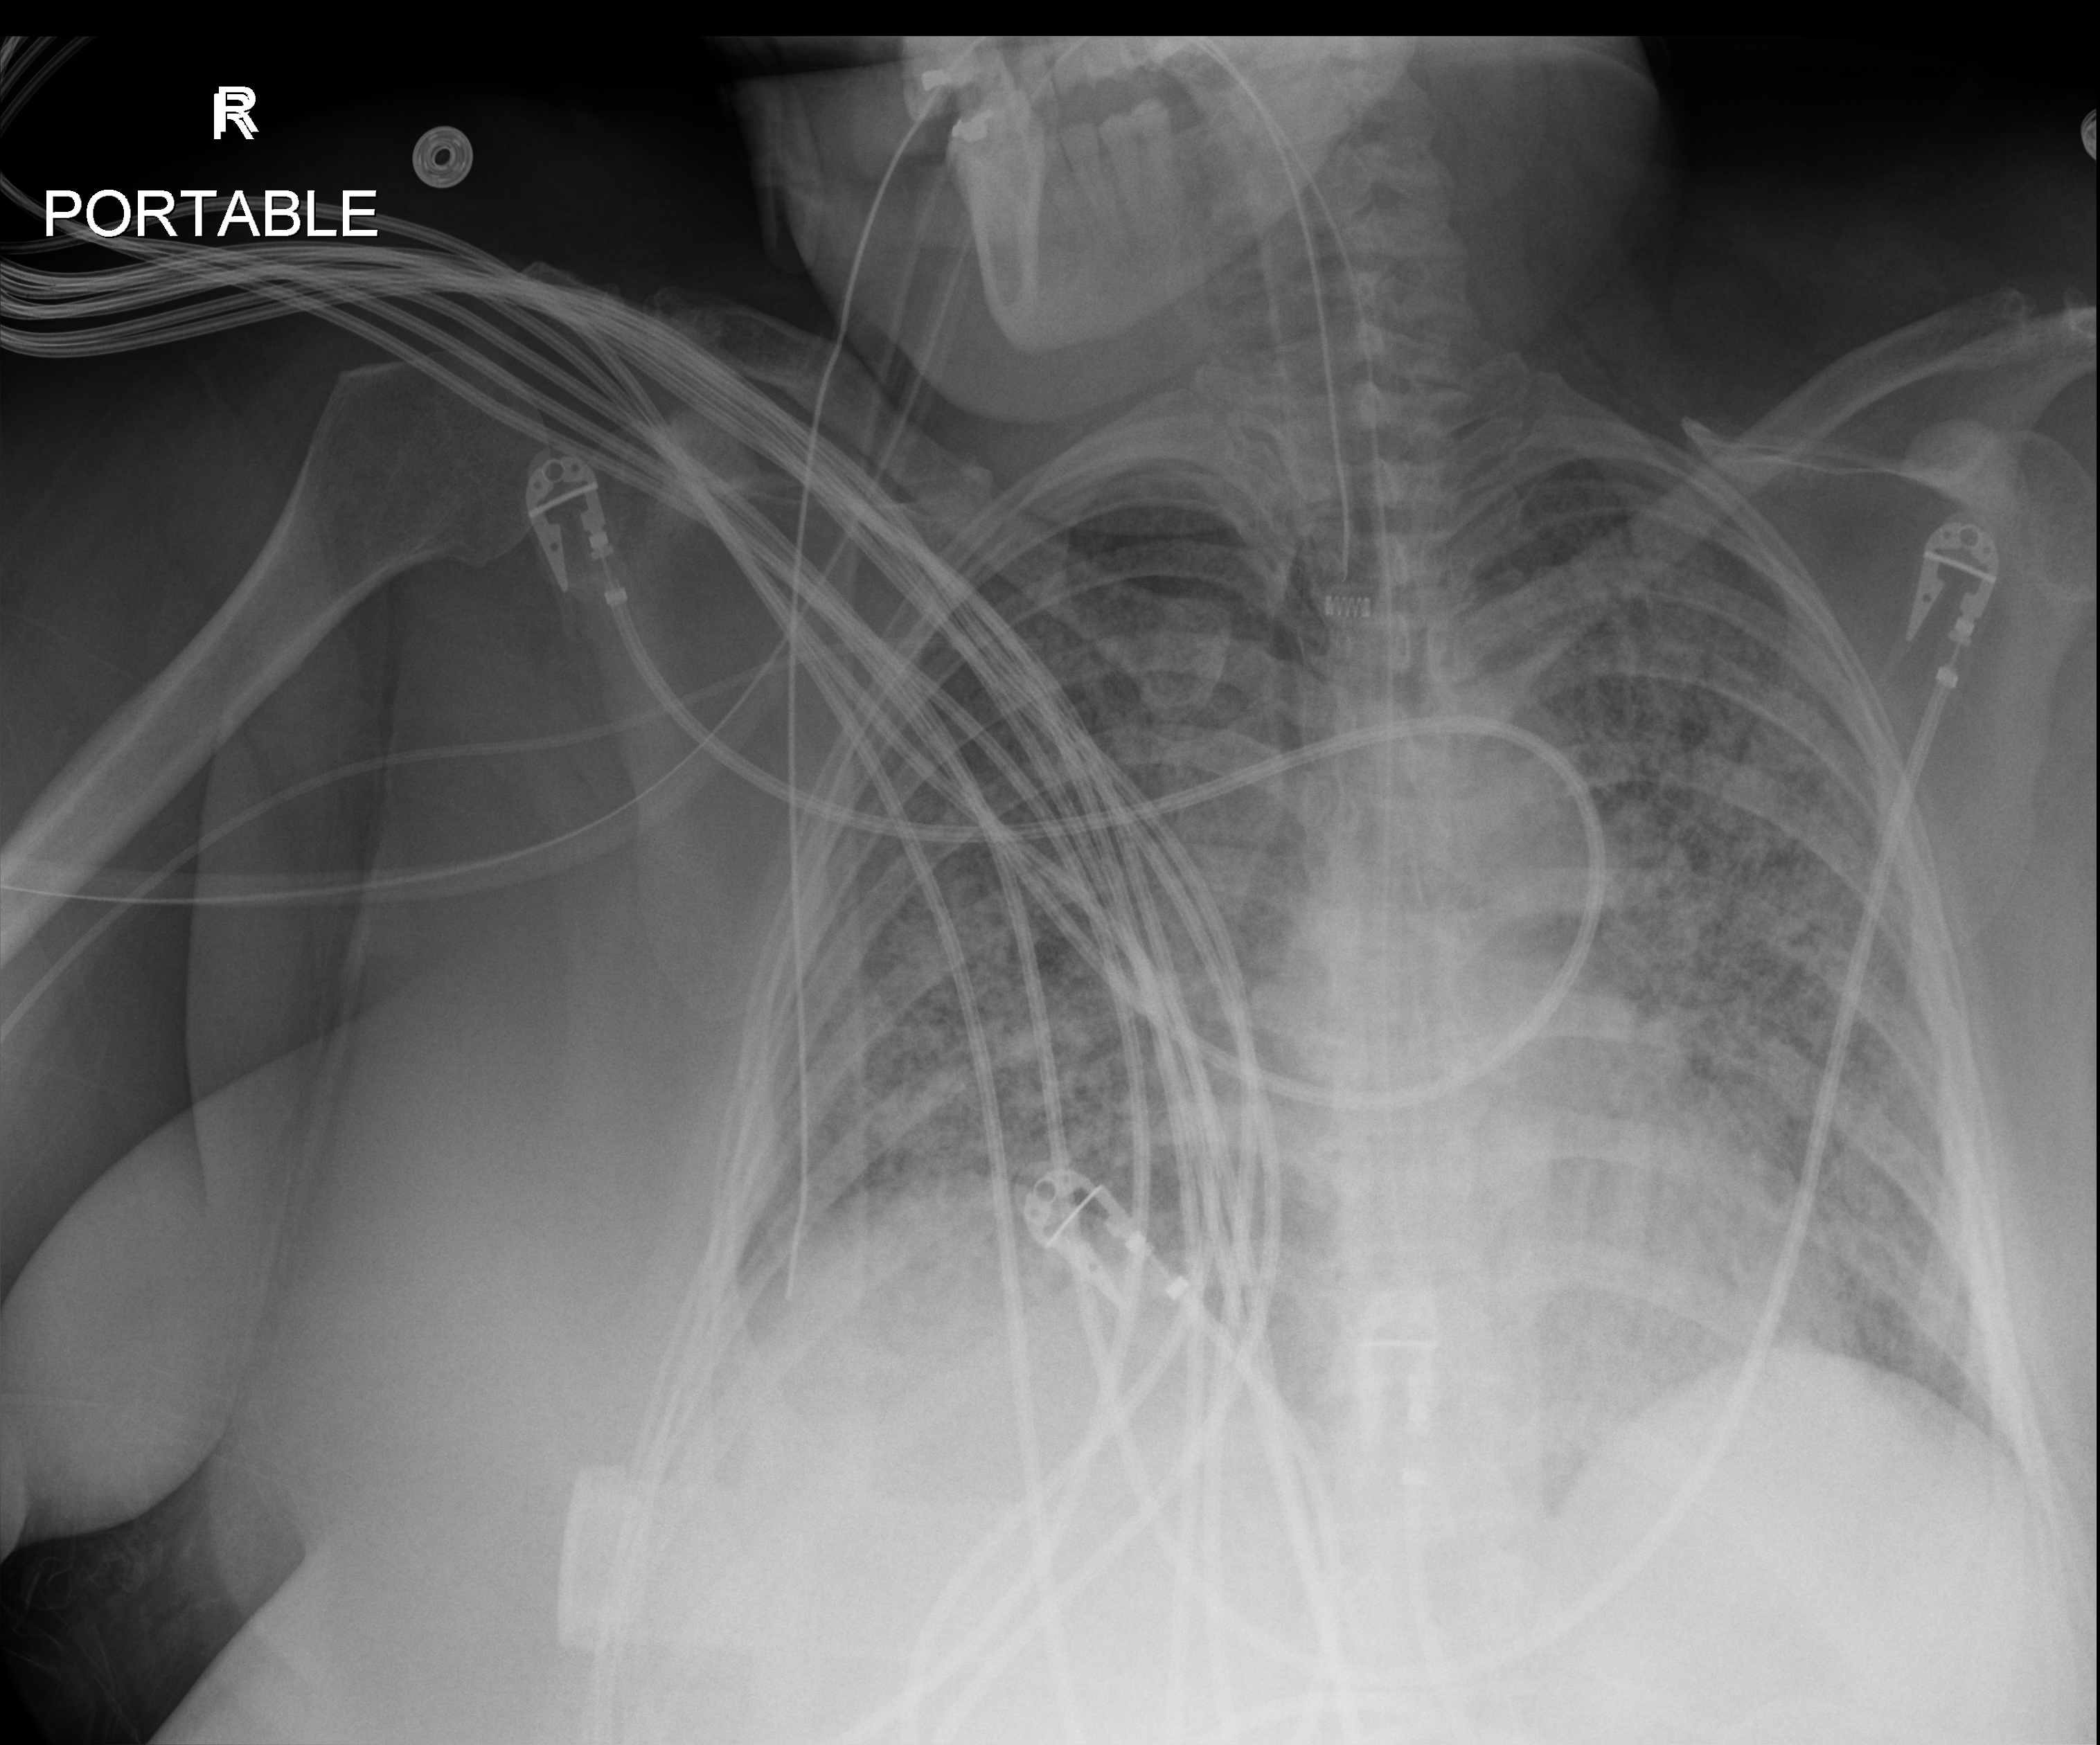
Chest X-ray (portable), anteroposterior (AP) projection. Female patient hospitalised with COVID-19, age 18–59 years.
Hospital-stay facts (about this admission, not read from this image; timing relative to this image not recorded):
- admitted to intensive care during this hospital stay: yes